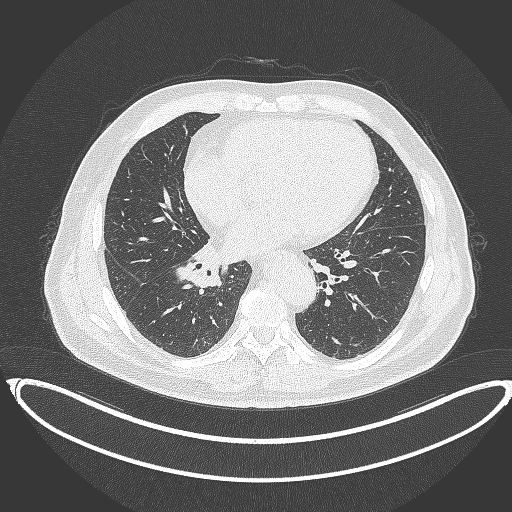
Chest CT, one axial slice; slice 171 of 387 in the series (ordered by position); reconstruction kernel B70f; 120 kVp; lung window (W 1500 / L -600 HU); 1 mm slice thickness; 512 × 512 image matrix, field of view 448 × 448 mm. Male patient, age 61 years. Case-level facts recorded for this patient, not image findings: clinical TNM (as recorded): T1b N1 M0.
Structures marked on this image (bounding box drawn by a radiologist):
- lung tumour (recorded histology: squamous cell carcinoma): bounding box [x1, y1, x2, y2] px = [175, 237, 222, 292]